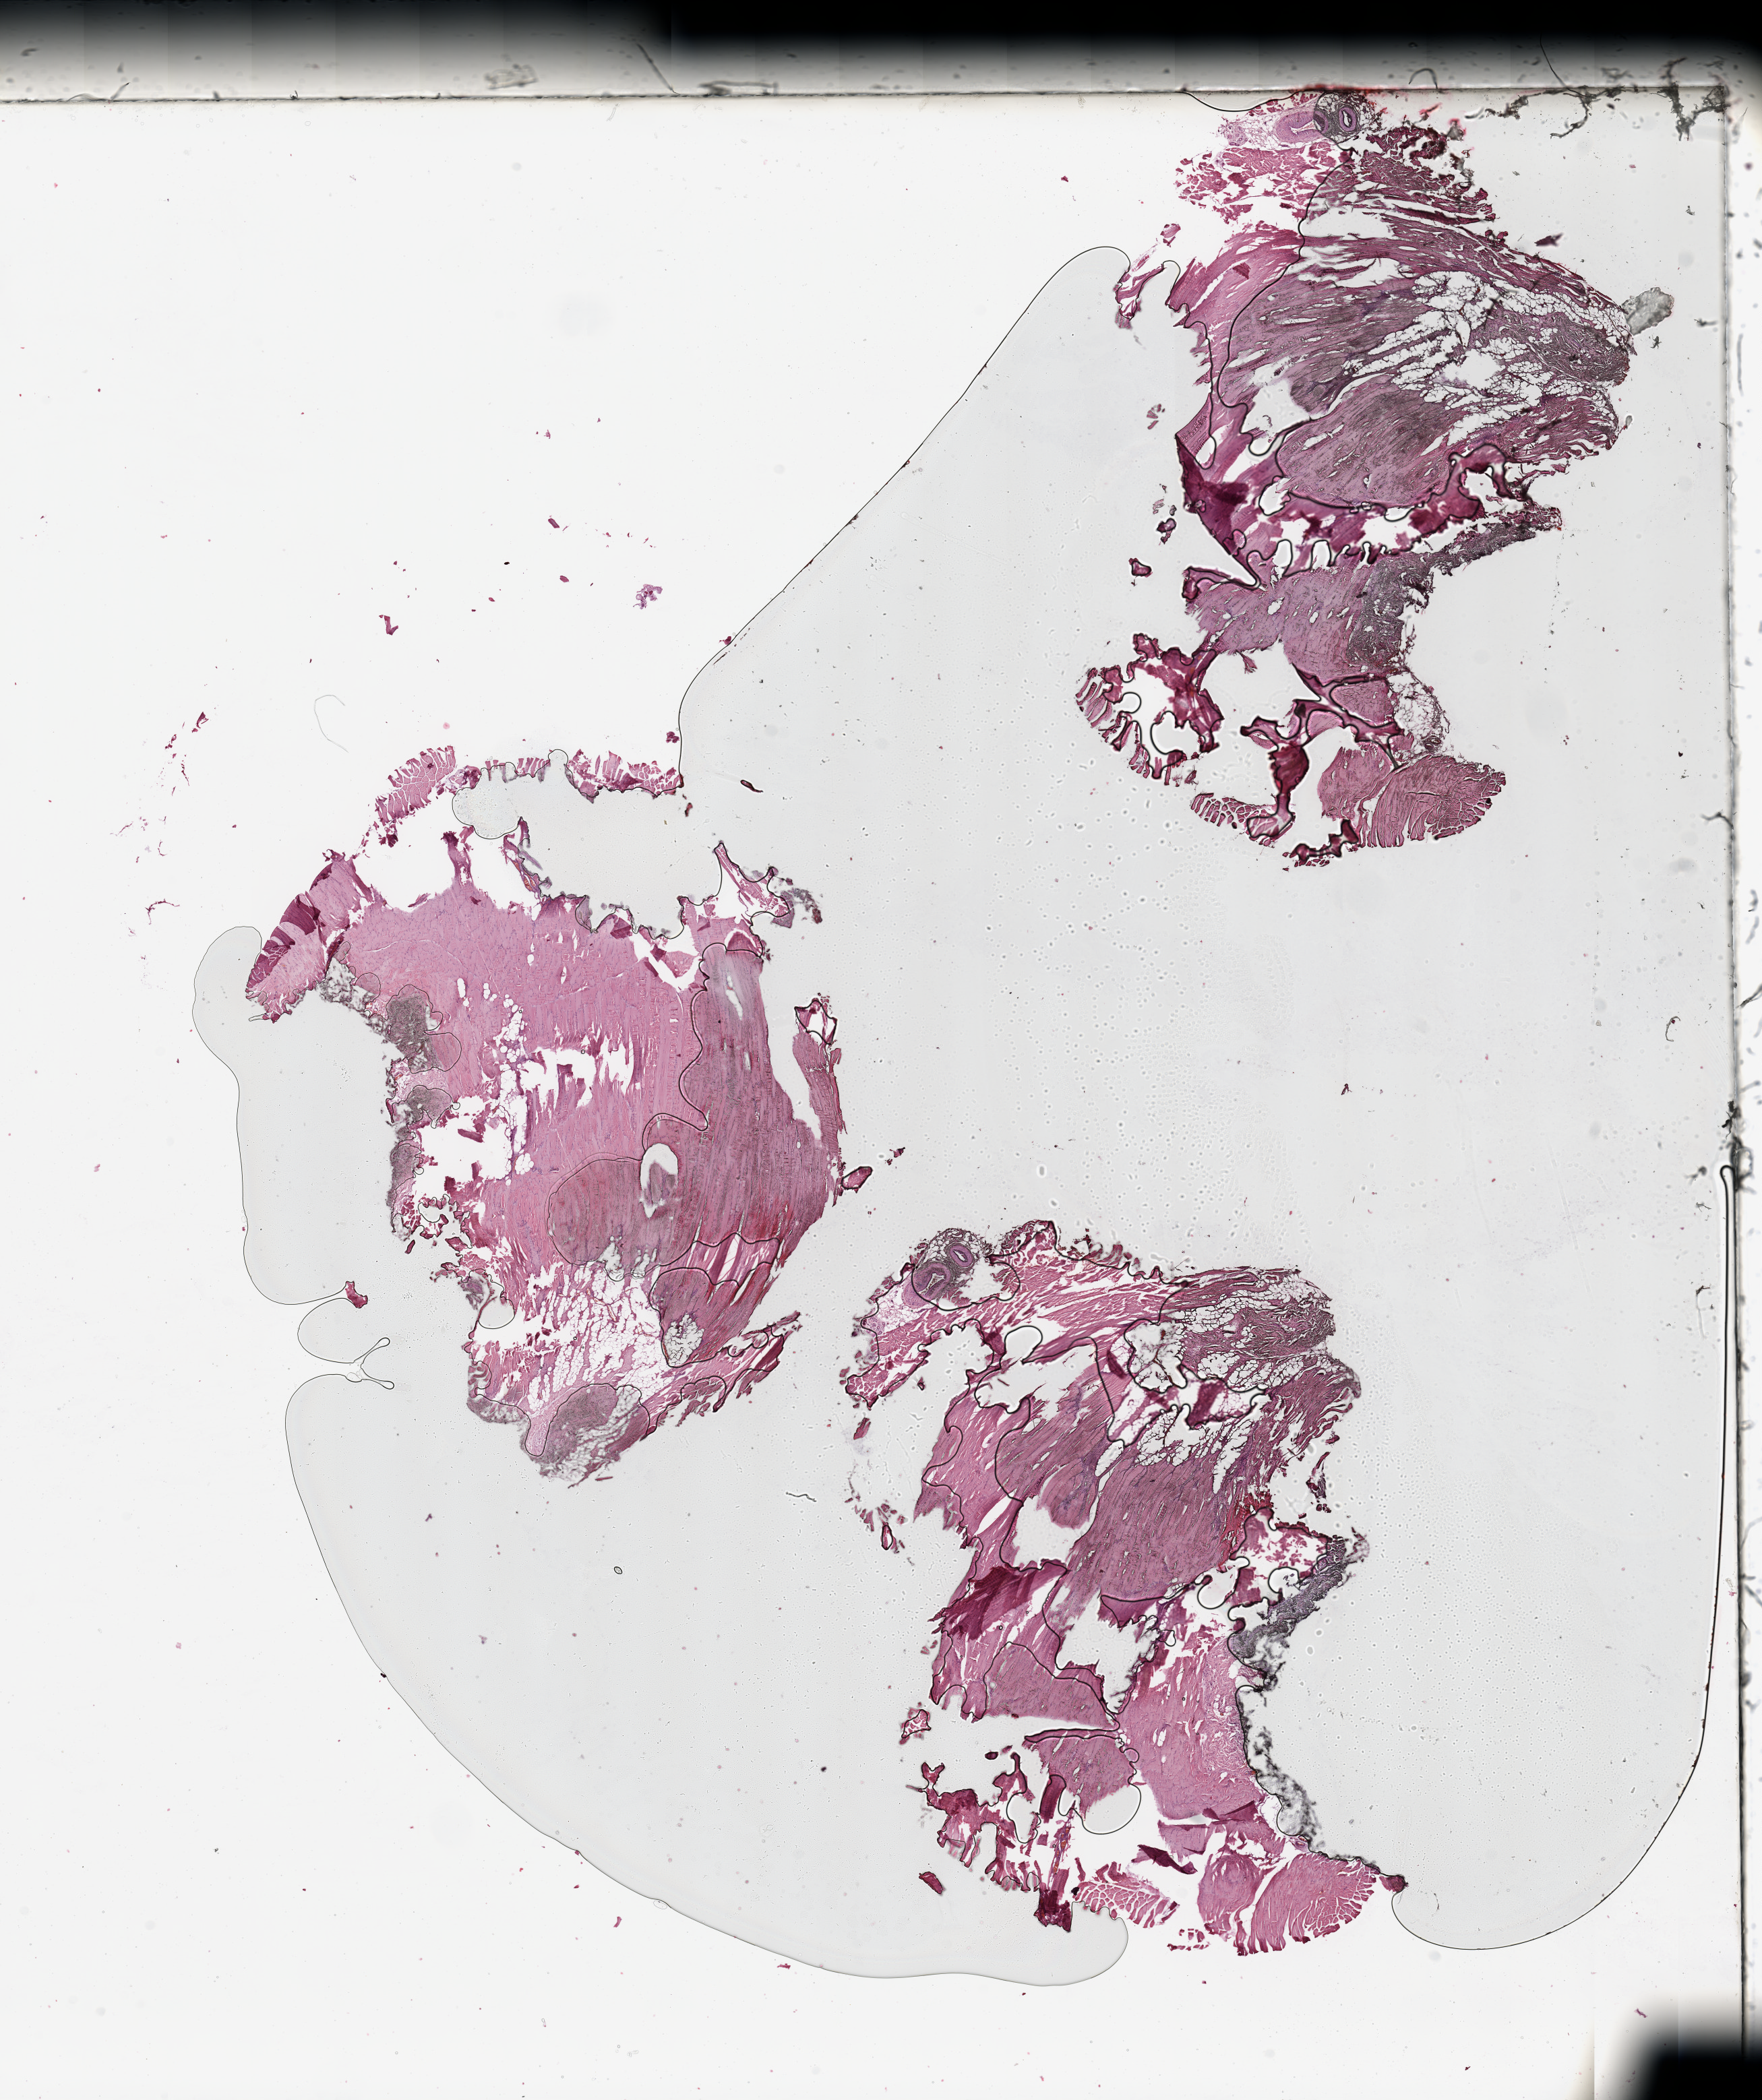
Whole-slide histology image, Hematoxylin and eosin (H&E) stained, a low-resolution overview of the entire scanned area, about 20.7 x 24.6 mm, normal (non-tumour) tissue sample. 52-year-old female patient.
This section: normal (non-tumour) tissue from the same patient. Patient diagnosis (cohort enrolment): sarcoma (site not recorded at cohort level).